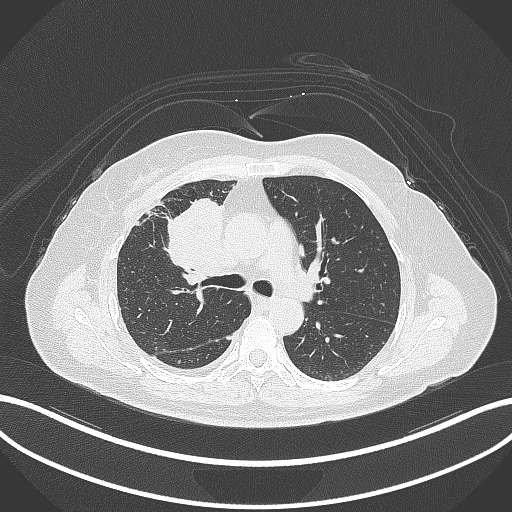
Chest CT, one axial slice; reconstruction kernel B70f; lung window (W 1500 / L -600 HU); 512 × 512 image matrix. Patient: female, 52 years. From the clinical record (not read from this slice): clinical TNM (as recorded): T3 N1 M1.
Outlined on this slice (rectangle marked by the reading radiologist):
- lung tumour (recorded histology: adenocarcinoma): box from (x=164, y=192) to (x=224, y=285) px